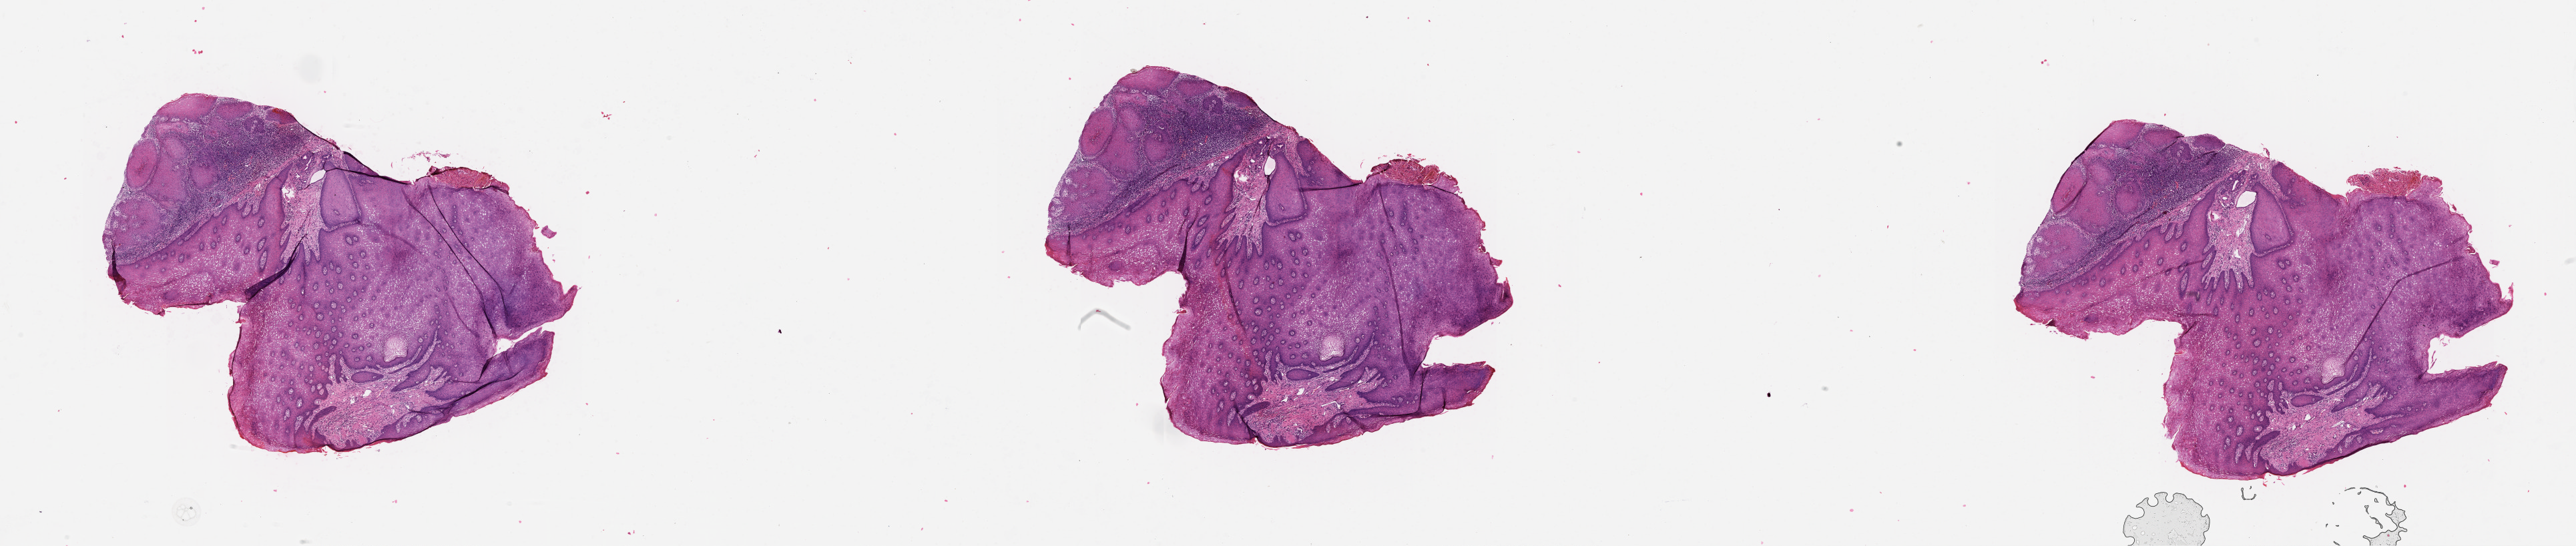
Whole-slide histology image, H&E-stained, a low-resolution overview of the entire scanned area, about 31.1 x 6.6 mm. Normal (non-tumour) tissue sample, sampled site: buccal mucosa. Patient: male, age 69 years.
This section: normal (non-tumour) tissue from the same patient. Patient diagnosis: Squamous cell carcinoma, NOS (cheek mucosa).